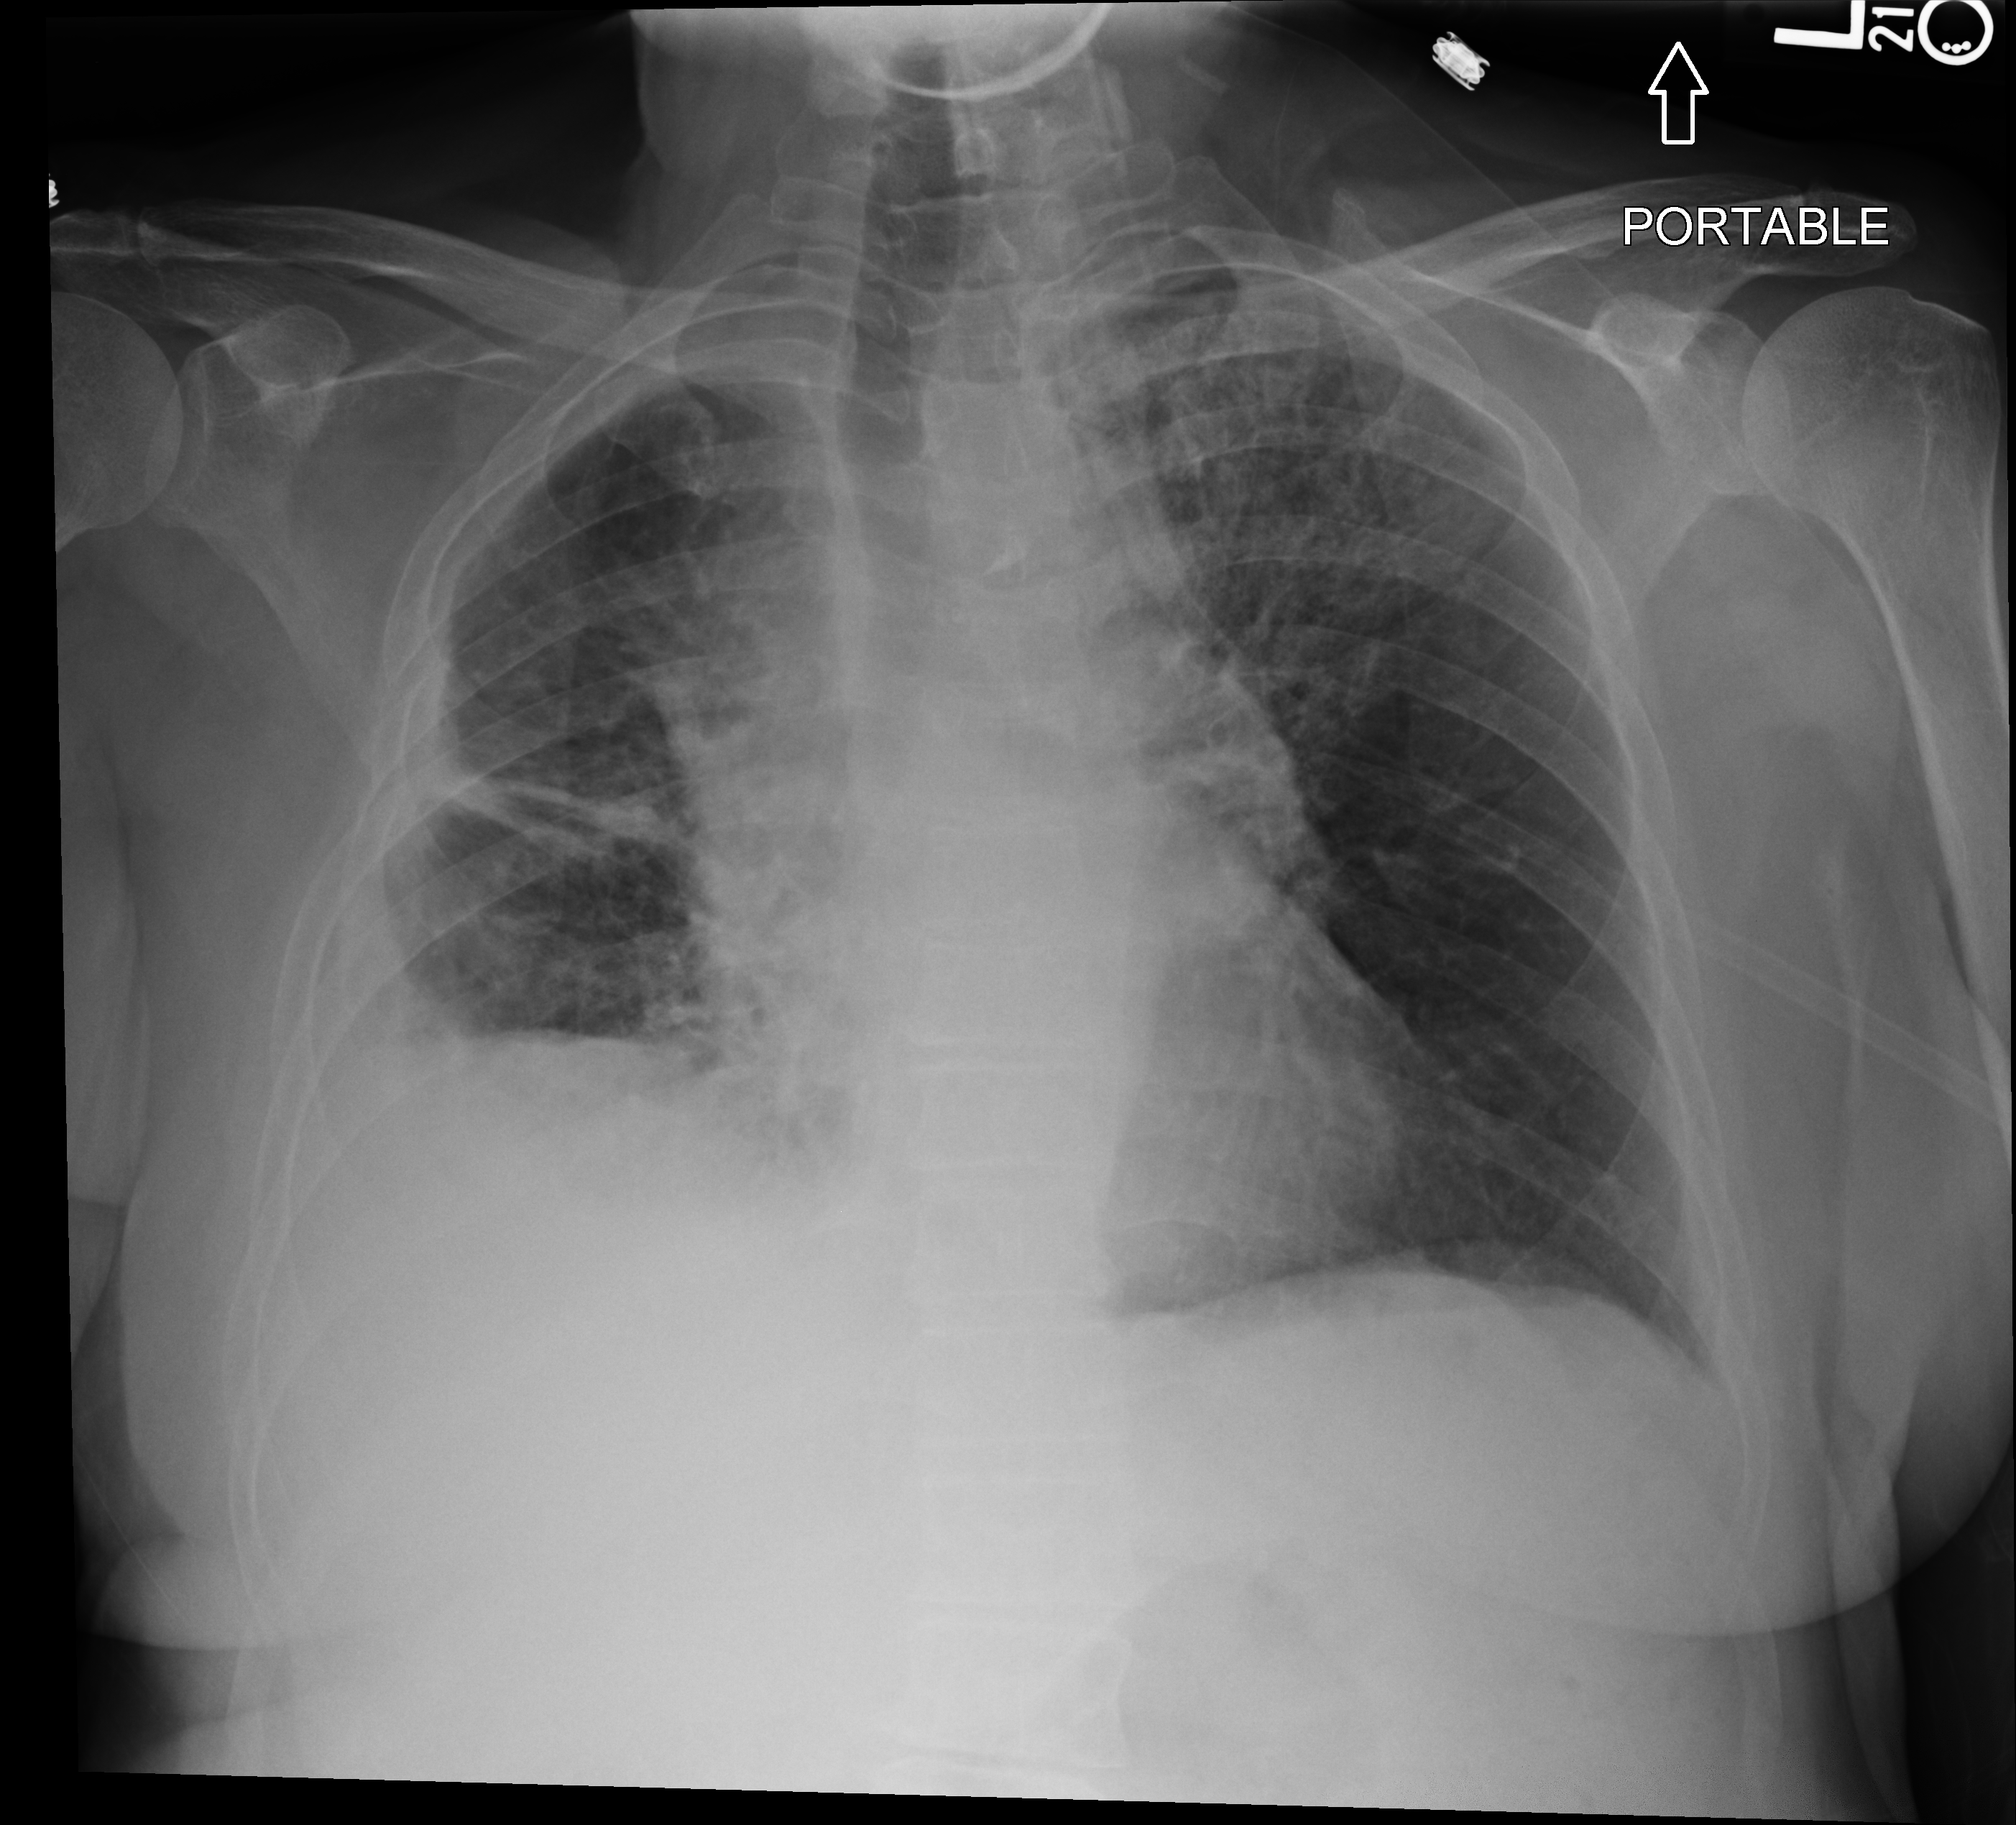
Bedside chest radiograph (computed radiography). Female patient hospitalised with COVID-19, age 60–74 years.
Hospital-stay facts (about this admission, not read from this image; timing relative to this image not recorded):
- length of hospital stay: 36 days